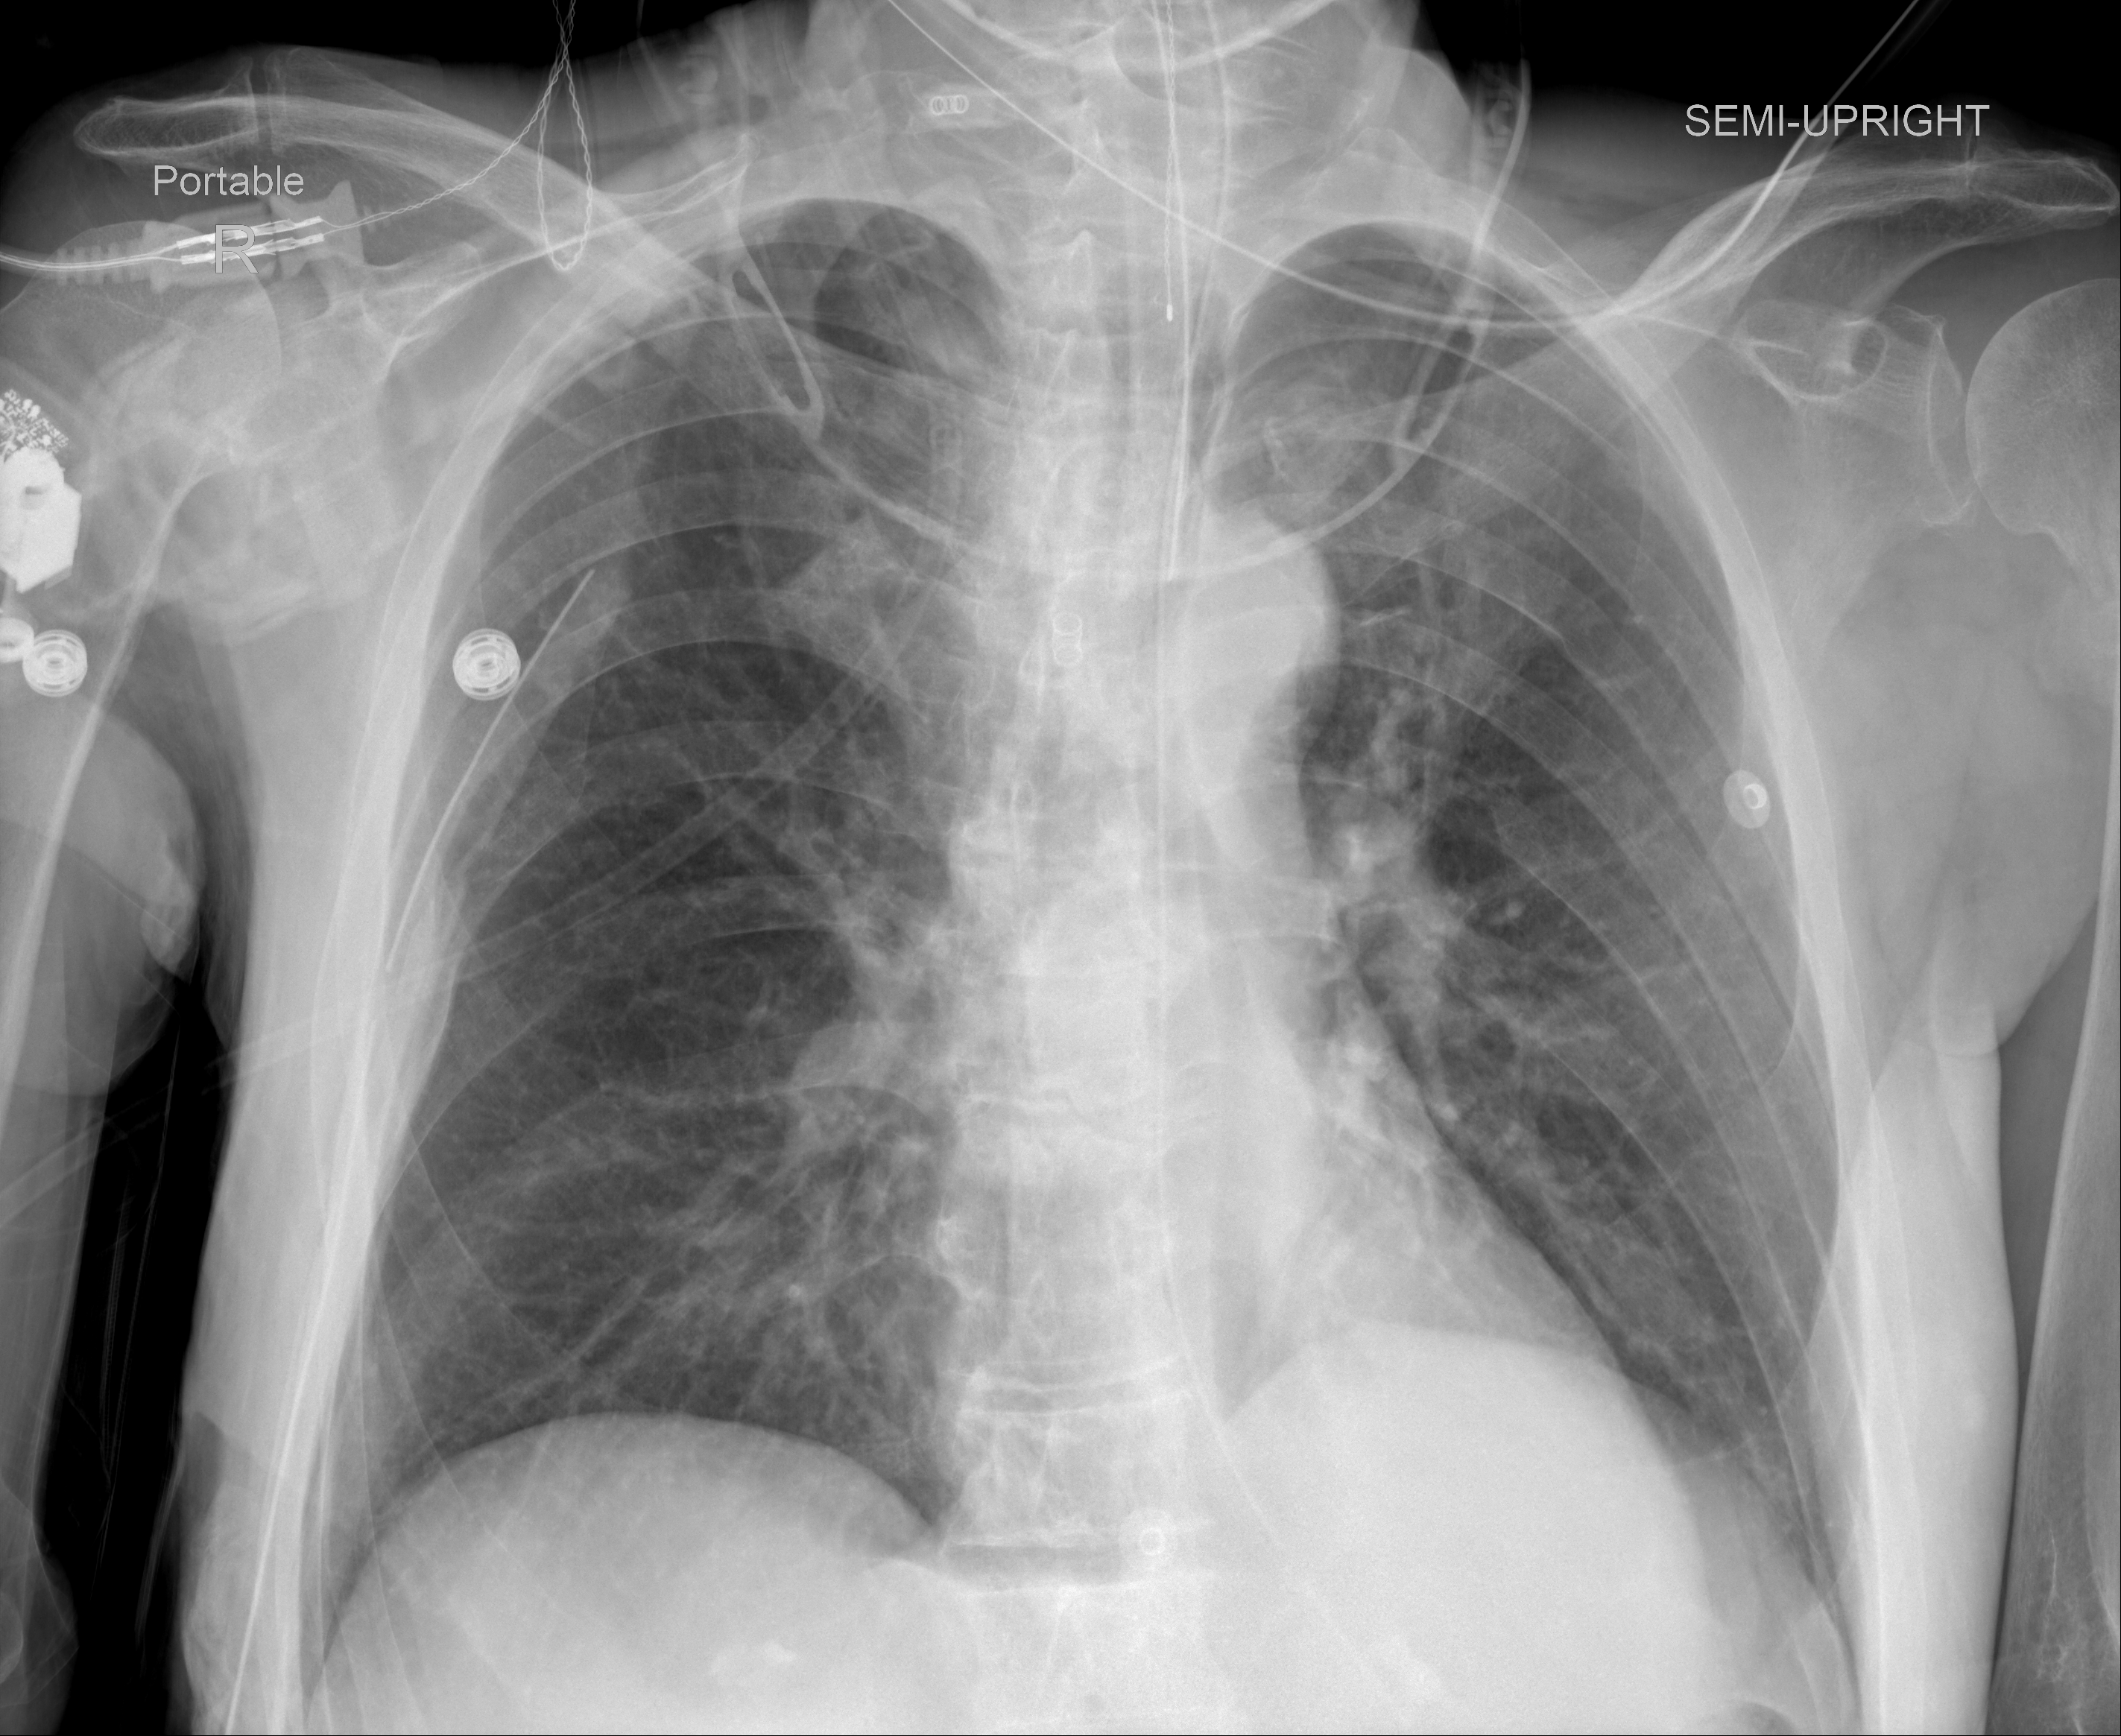
Chest X-ray (portable), AP projection. Male patient, age 59 years; imaged 1 day after the COVID-19 diagnosis.
Radiologist's key findings for this exam: The lungs remain clear. No pleural effusion.